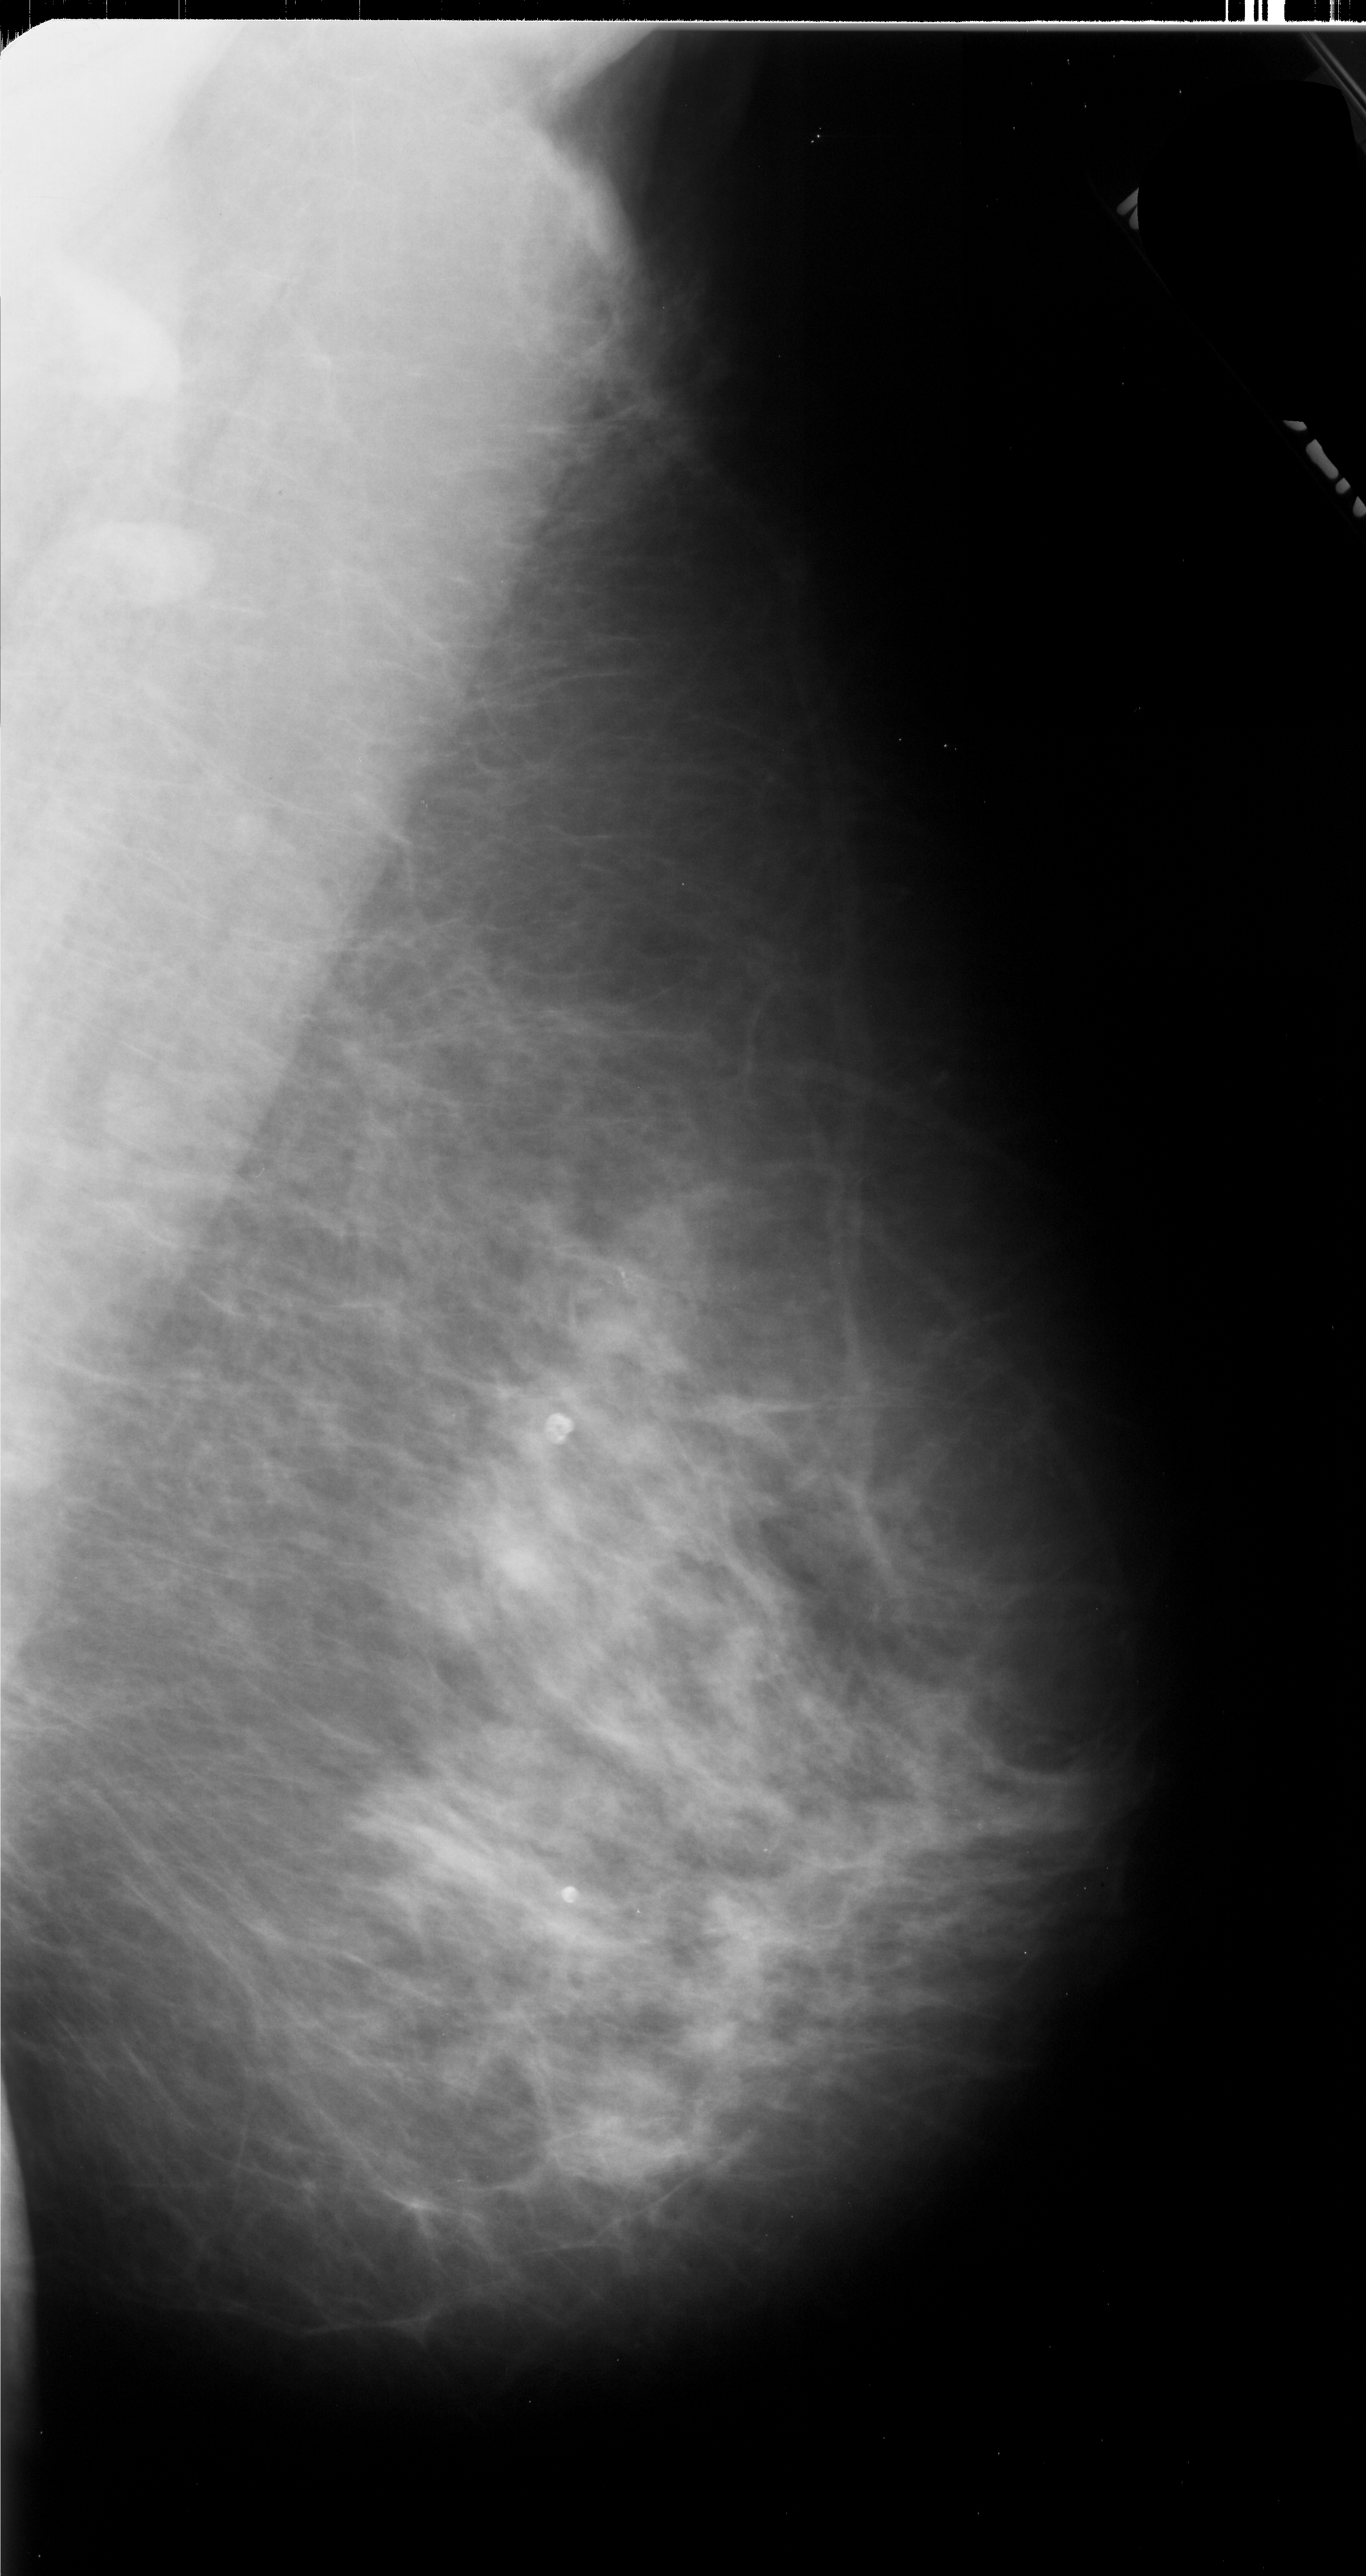
Mammogram (digitized film). Right breast. MLO view. BI-RADS breast density category 3 (scale 1–4). 1366 × 2576 image matrix.
Expert-marked regions of interest on this film, with their recorded descriptors:
- calcifications, morphology pleomorphic, distribution linear; BI-RADS assessment category 4; pathology result (as recorded, not read from the image): malignant: bounding box (x1, y1, x2, y2) in pixels: (580, 1232, 760, 1337)